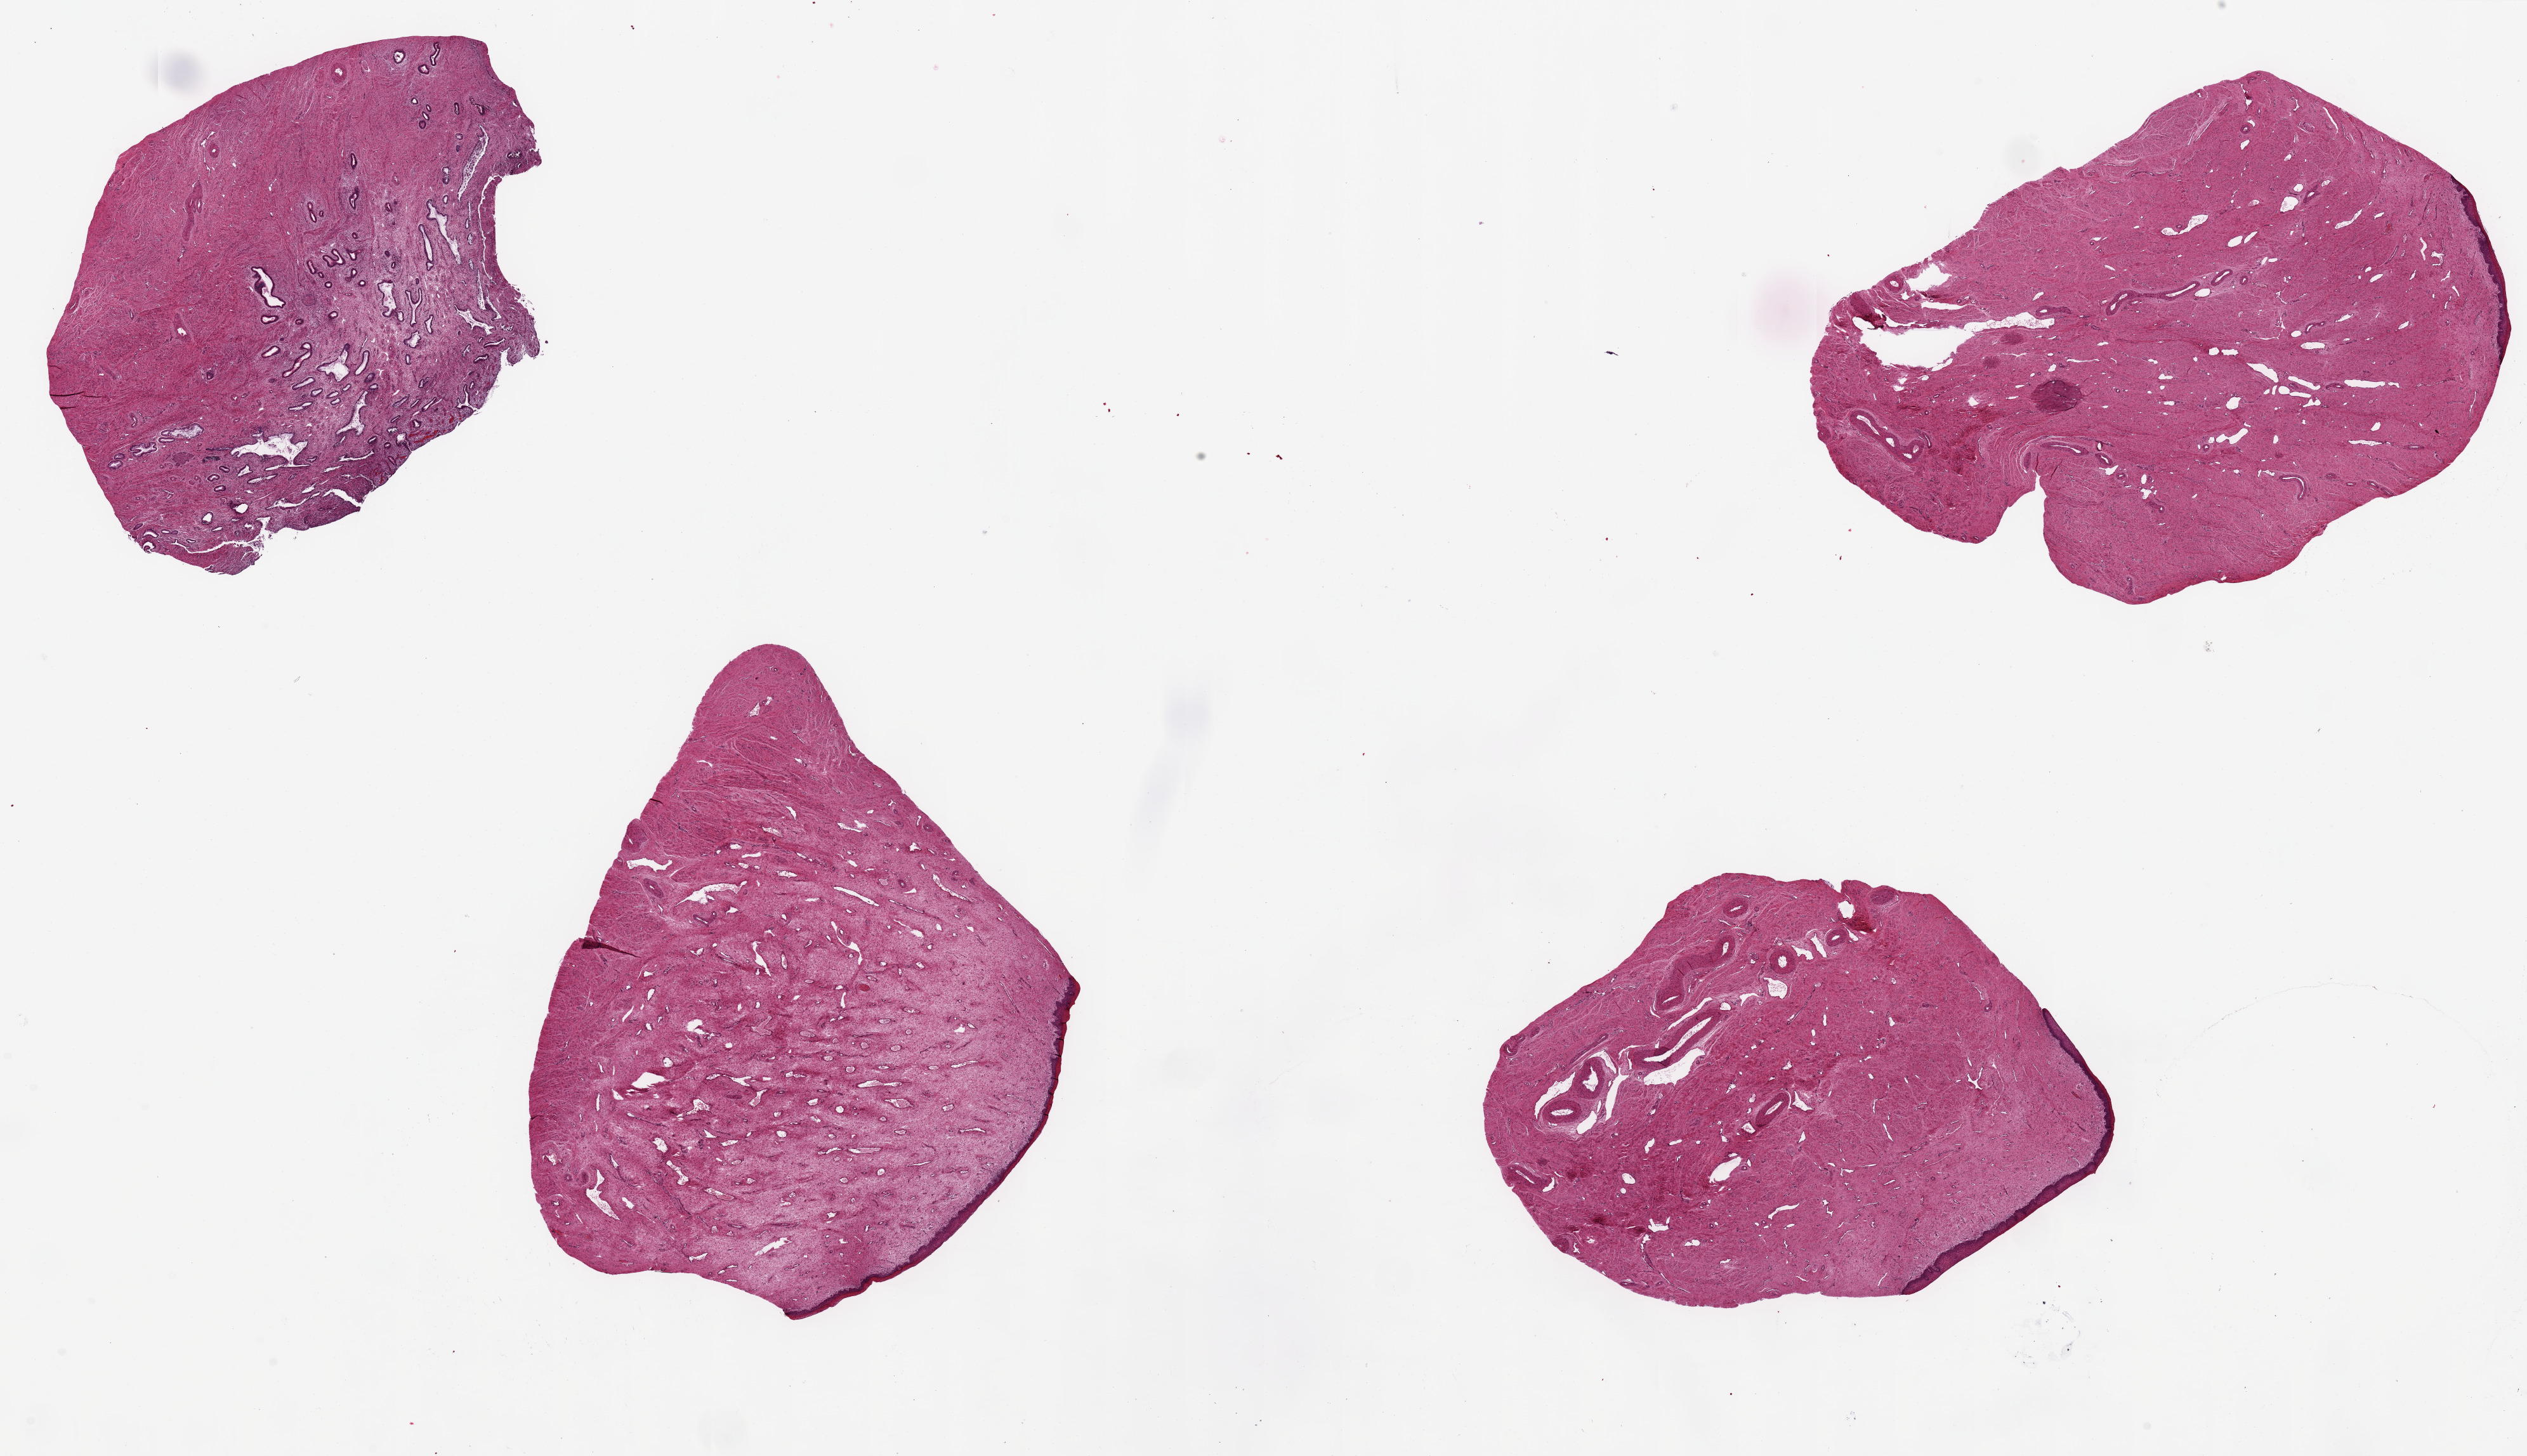
H&E whole-slide image, brightfield — a low-resolution overview of the entire scanned area, about 31.5 x 18.2 mm (from a 20x scan). PAXgene-fixed, paraffin-embedded tissue. Sampled site (target tissue): endocervix. Tissue donor sample. Female donor.
Pathologist's review note for this sample: 4 pieces, ~6x7mm, 3 ectocervix focally atrophic surface, 1 piece endocervix.